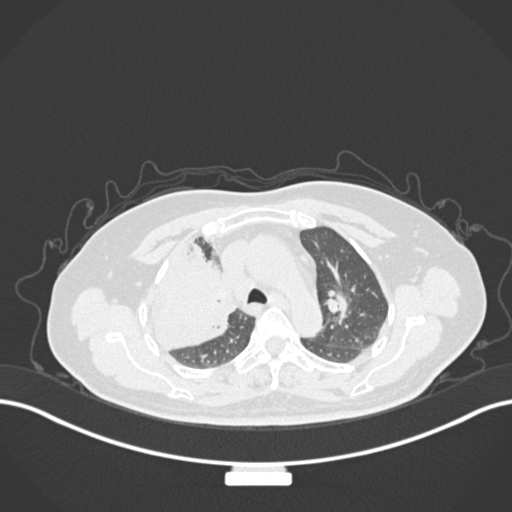
Chest CT, one axial slice; position 110 of 177 along the scan axis; 120 kVp; lung window (W 1500 / L -600 HU); 1 mm slice thickness; 512 × 512 image matrix, field of view 400 × 400 mm. Female patient, age 60 years. From the clinical record (not read from this slice): clinical TNM (as recorded): T3 N1 M1.
Outlined on this slice (bounding box drawn by a radiologist):
- lung tumour (recorded histology: adenocarcinoma): box from (x=148, y=243) to (x=237, y=358) px